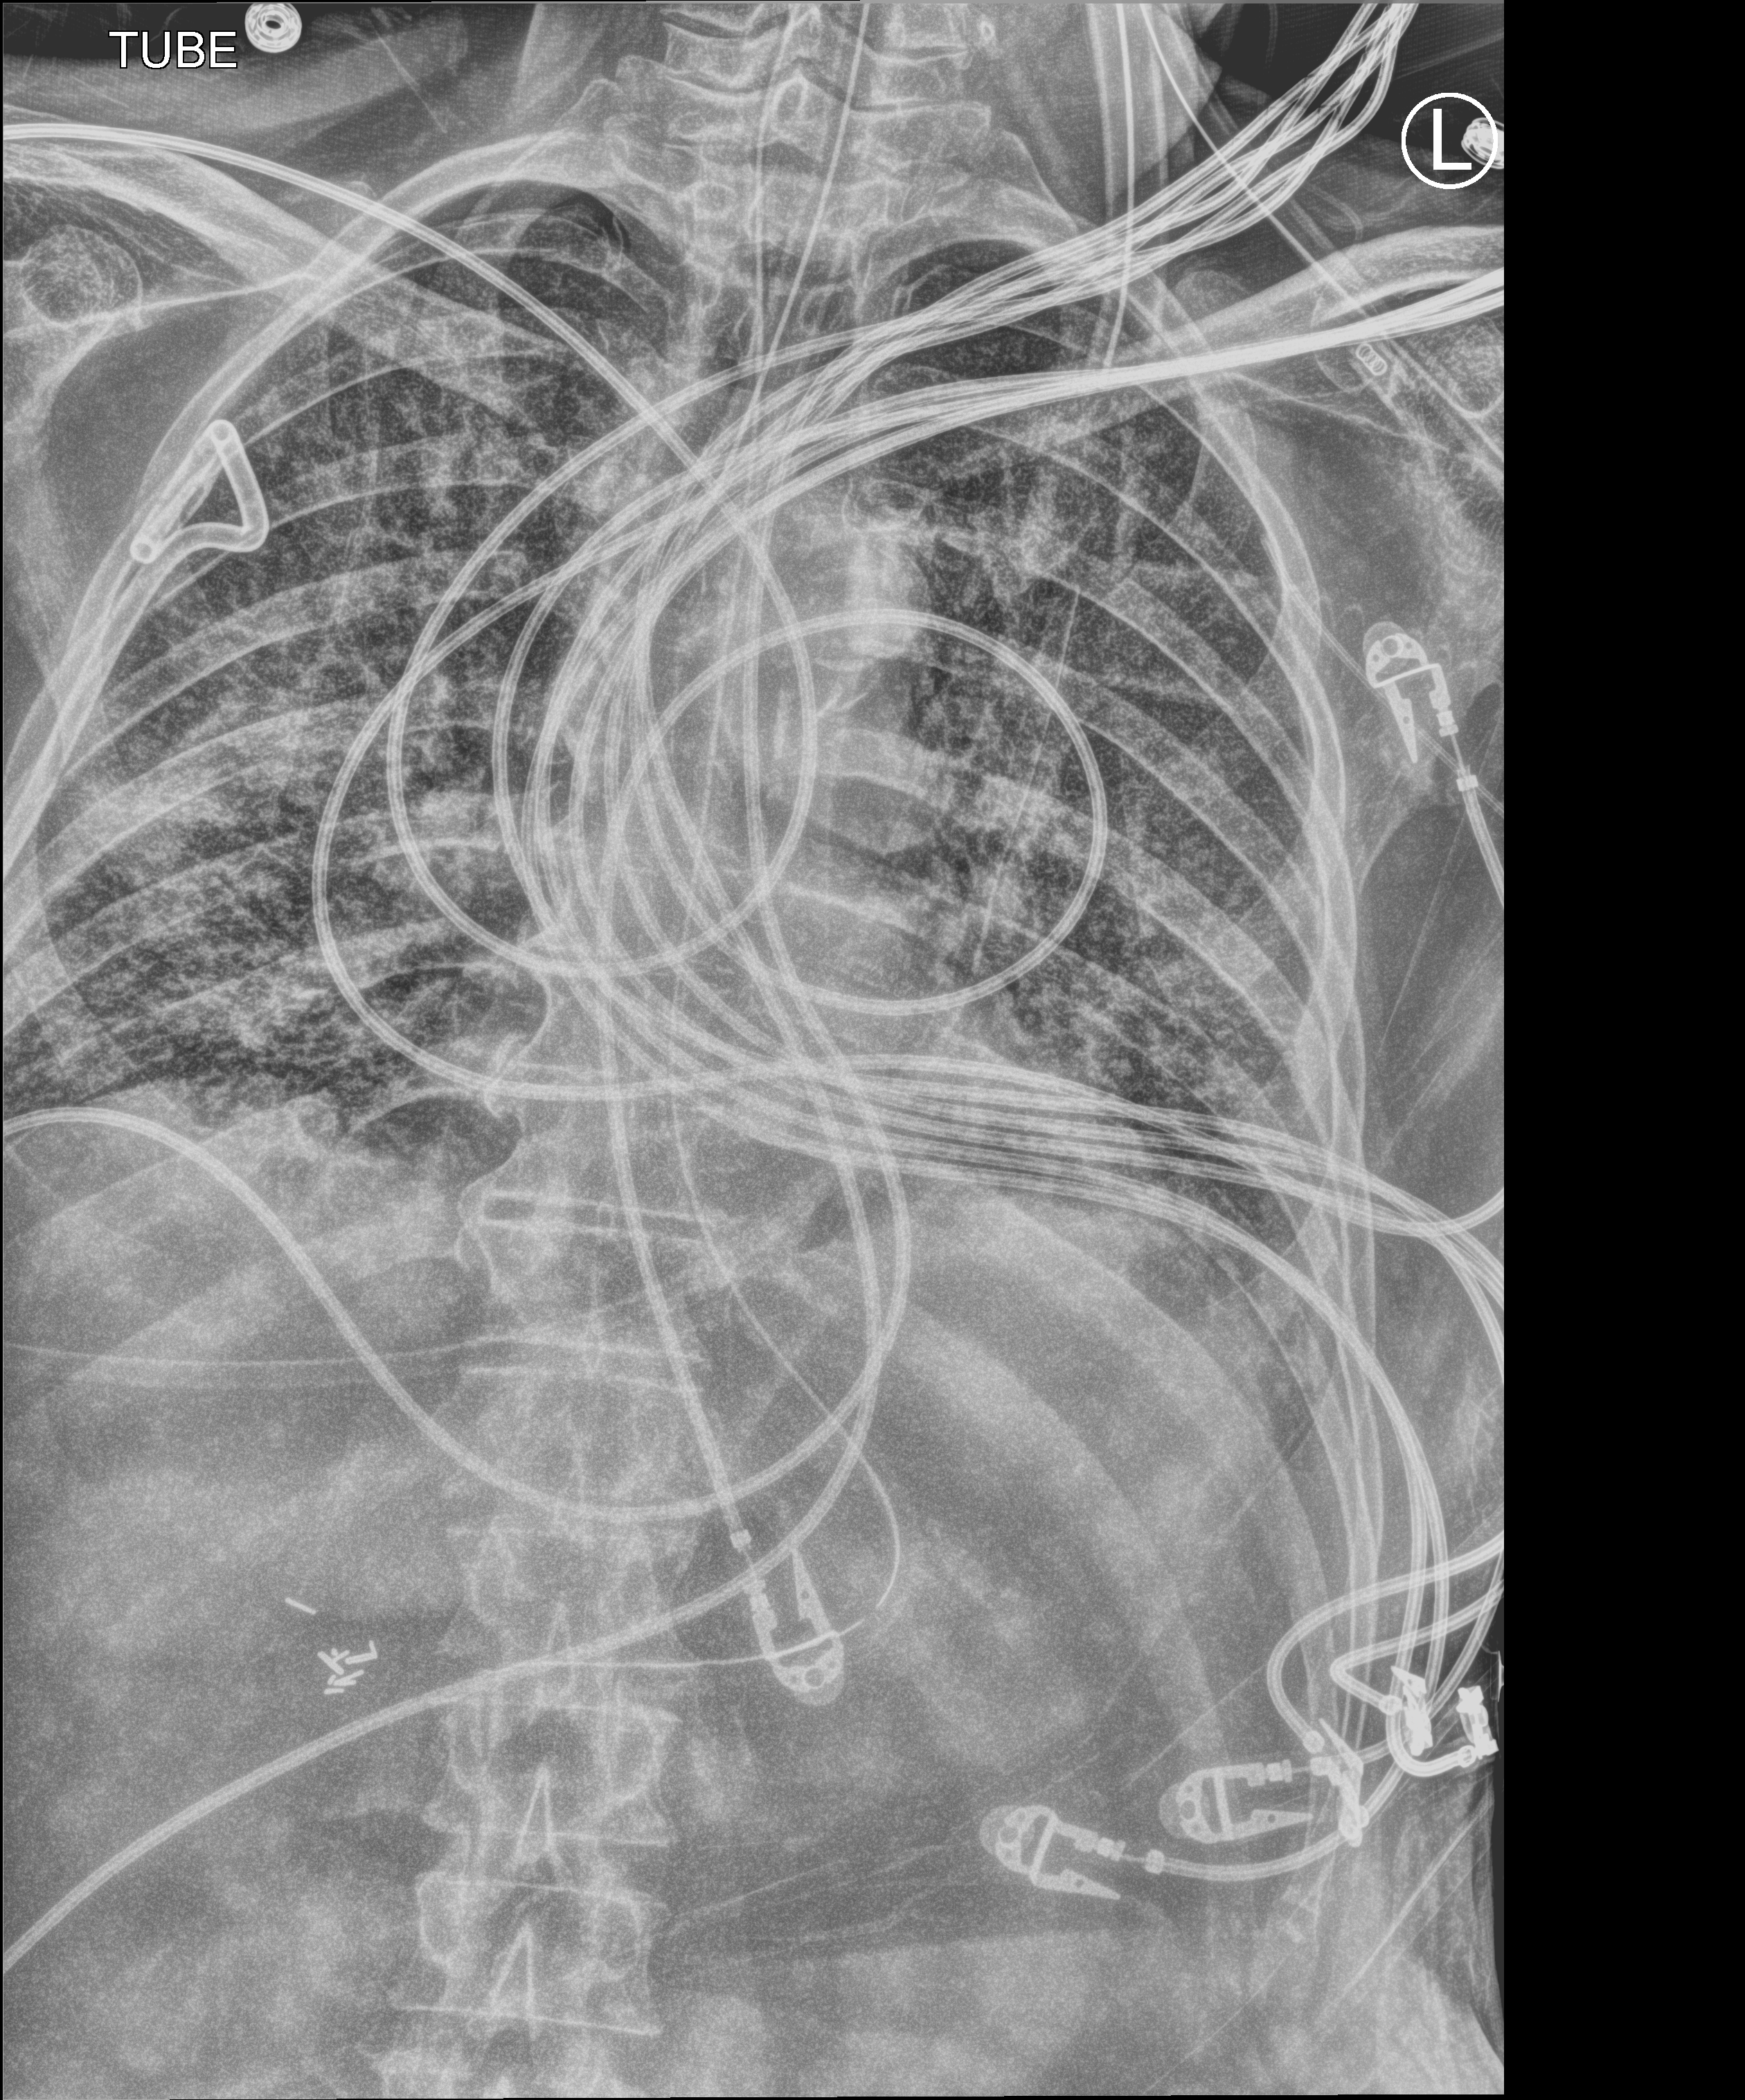
Bedside chest radiograph (computed radiography); anteroposterior (AP) projection. Patient hospitalised with COVID-19; male, aged 75–90 years.
Hospital-stay facts (about this admission, not read from this image; timing relative to this image not recorded):
- mechanically ventilated during this hospital stay: yes
- hypertension (admission record): yes